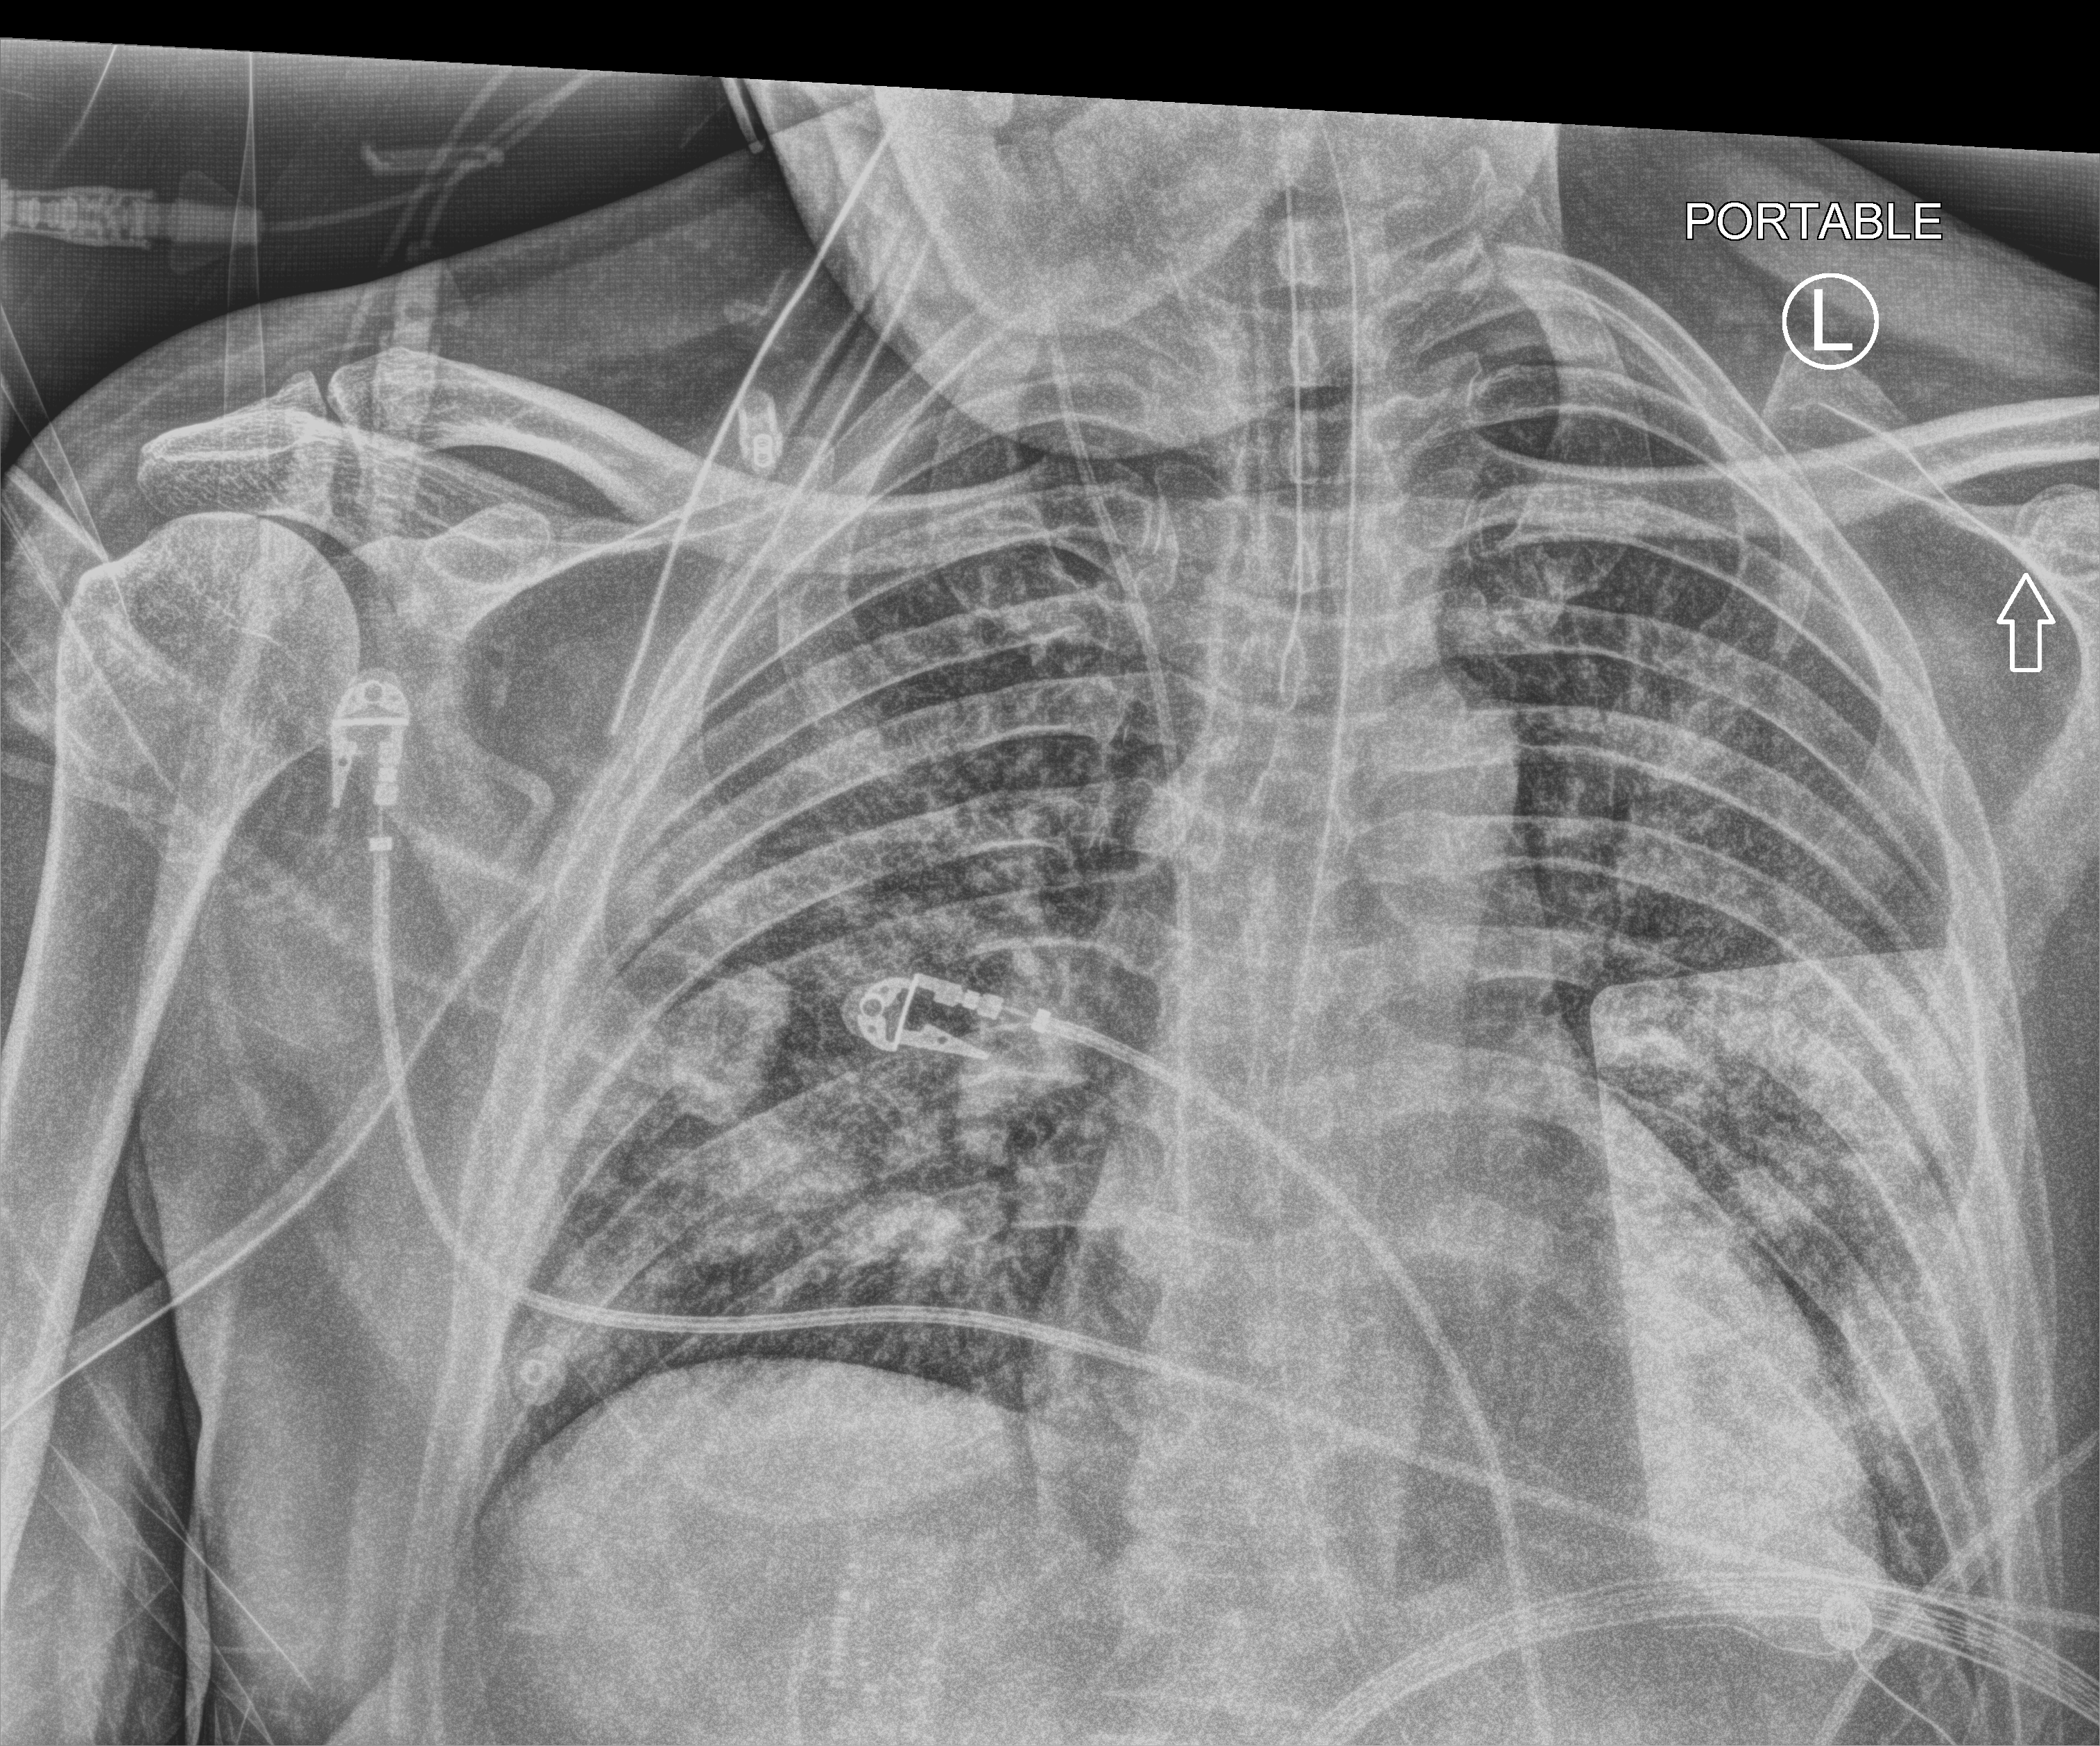
Portable chest radiograph, anteroposterior (AP) projection. Male patient hospitalised with COVID-19, age 18–59 years.
Hospital-stay facts (about this admission, not read from this image; timing relative to this image not recorded):
- length of hospital stay: 75 days